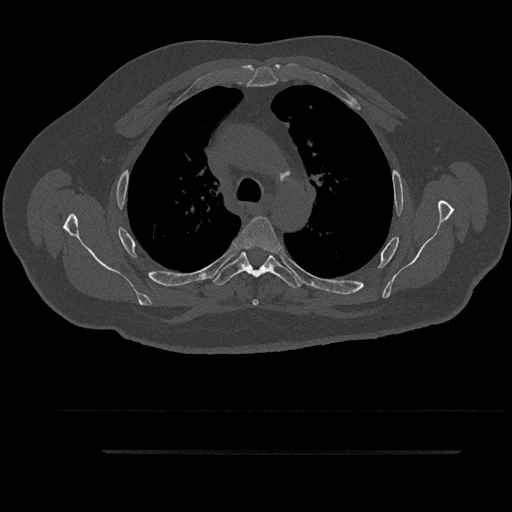
CT including the spine, one axial slice. Reconstruction kernel Br40s/3. 120 kVp. Bone window (W 1800 / L 400 HU). 0.5 mm slice thickness. 512 × 512 image matrix. Patient: male, 63 years. From the clinical record (not read from this slice): primary cancer: renal.
Annotated regions visible in this slice (semi-automatic segmentation, software-assisted and operator-edited):
- T3 vertebra: bounding box [x1, y1, x2, y2] px = [266, 257, 270, 263]
- T4 vertebra: [236, 216, 282, 306]
- T5 vertebra: [214, 249, 300, 290]